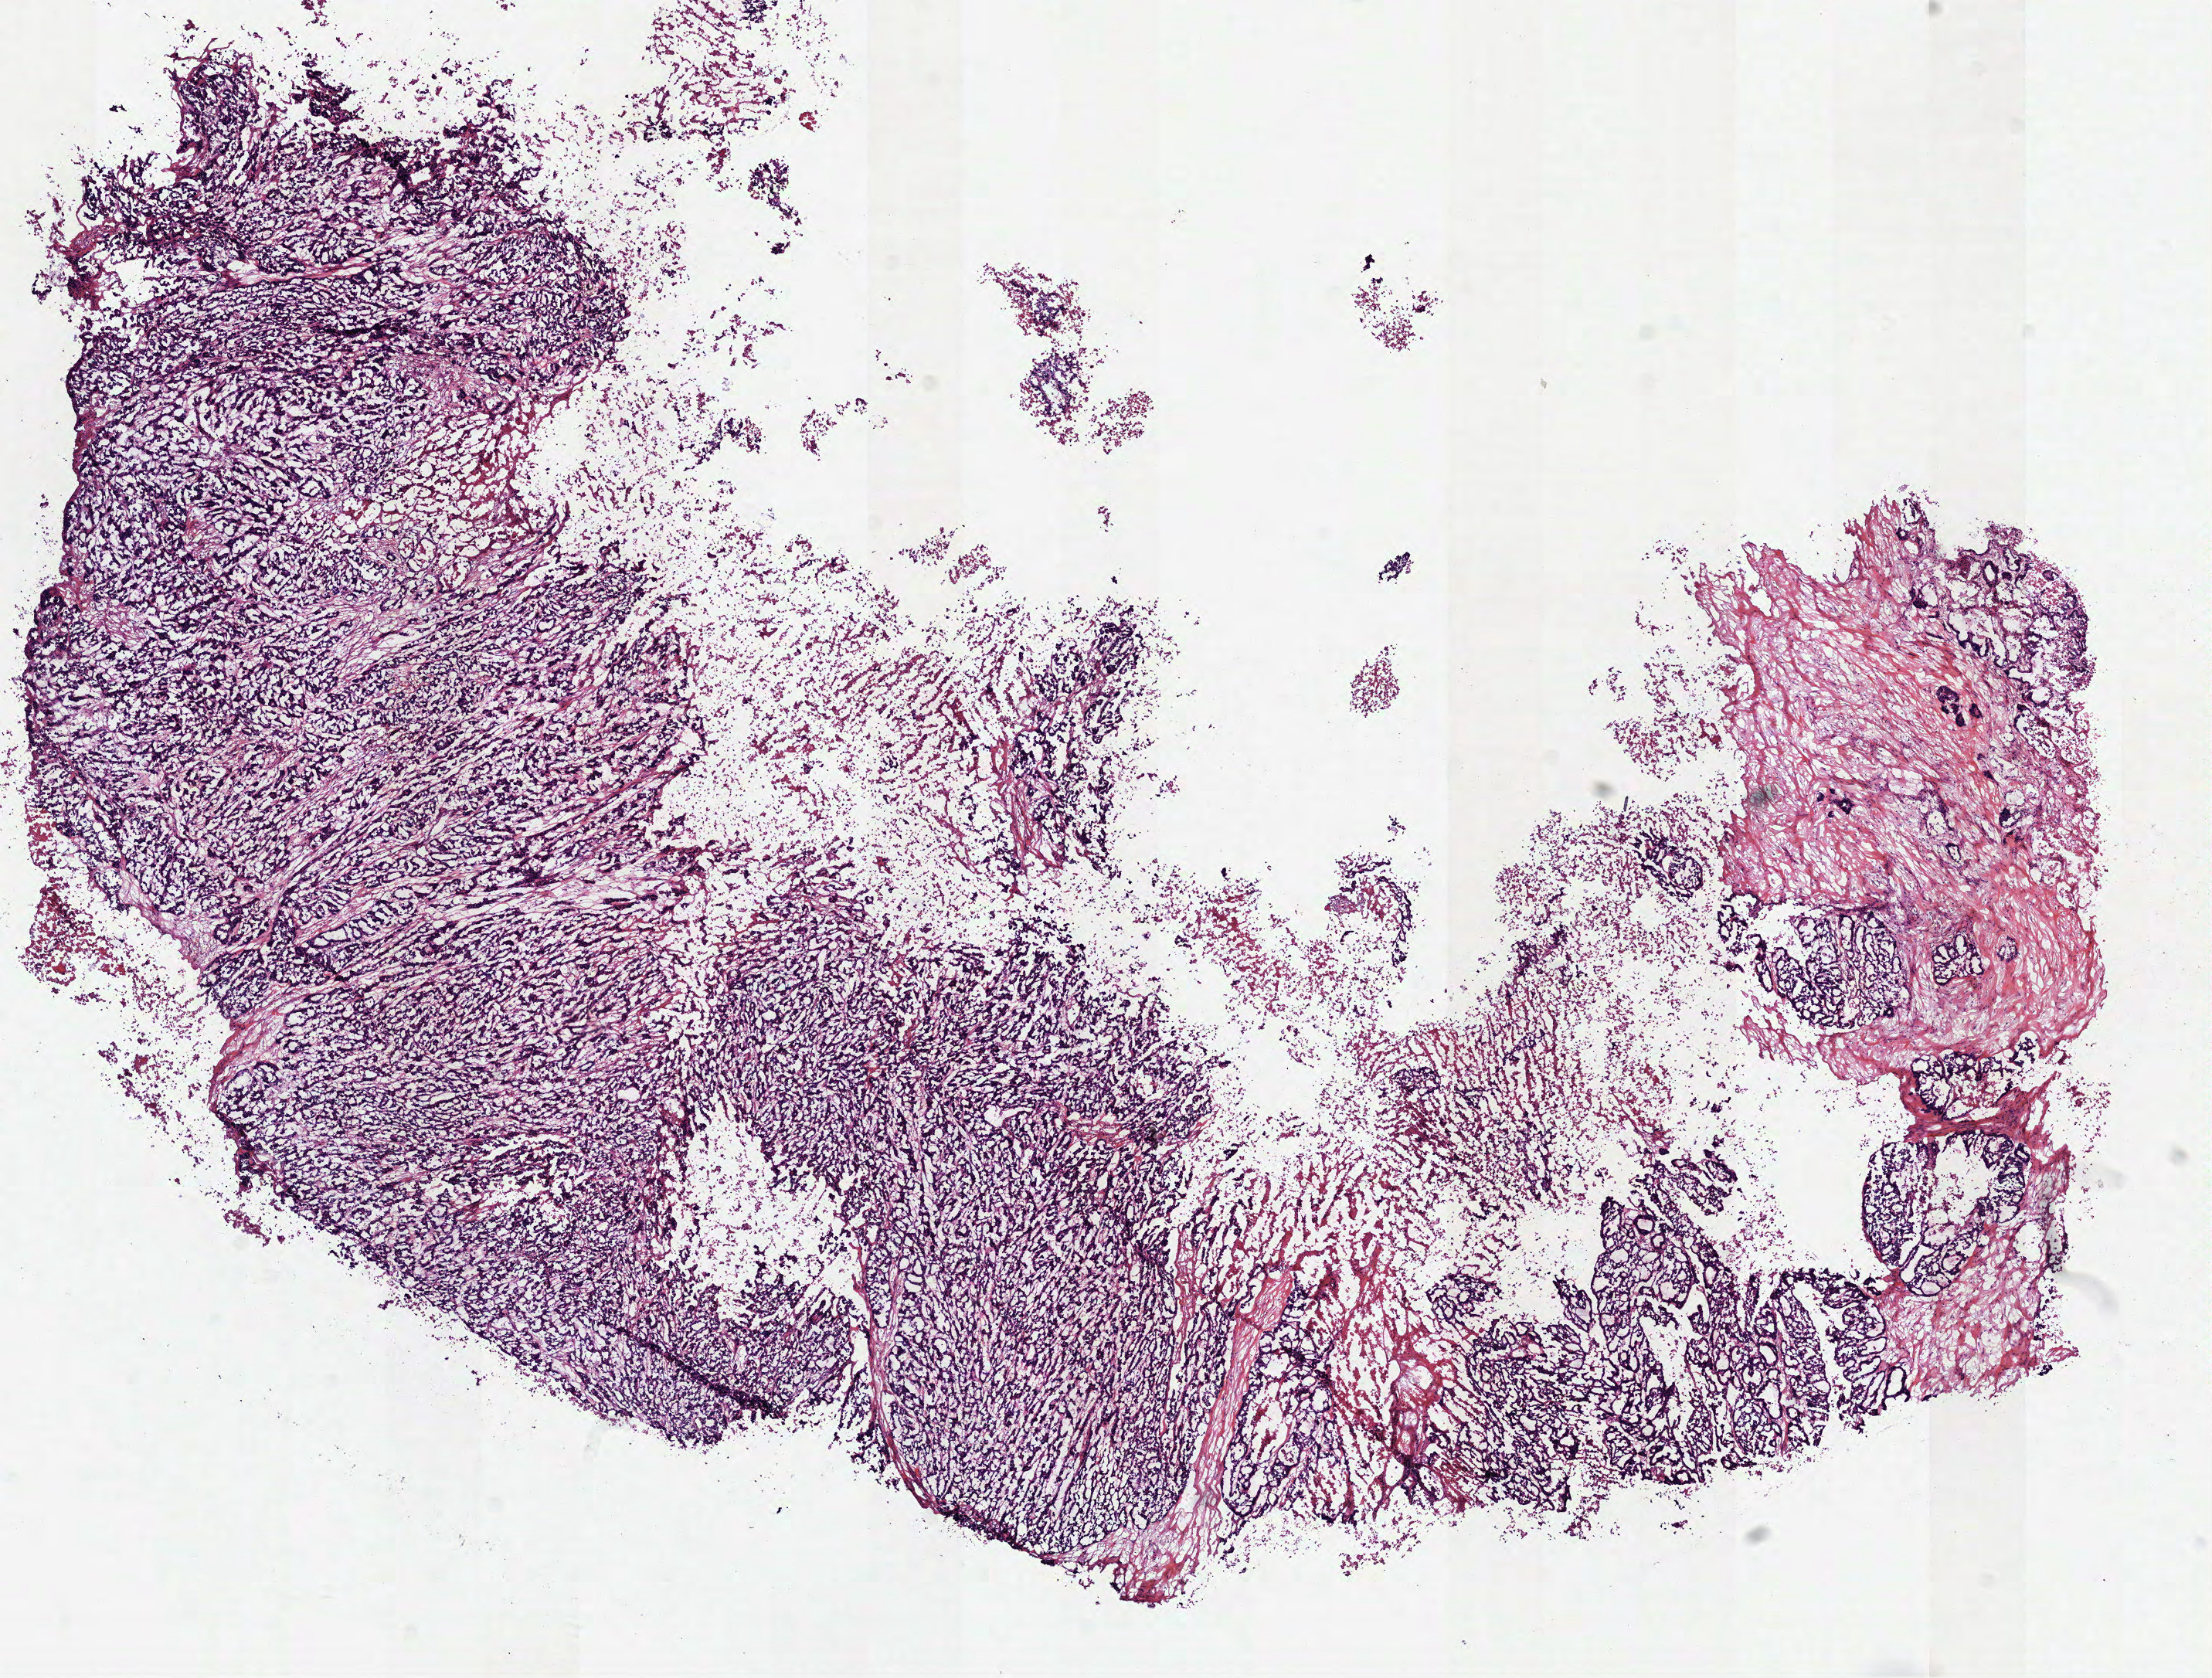
Digitized Hematoxylin and eosin (H&E) stained tissue section (whole slide), whole scanned area (about 11.5 x 8.8 mm) shown as a low-resolution overview; frozen section from the top of the tissue portion; primary tumour sample from the stomach. Patient: male, age at initial diagnosis 59 years. Histologic grade: G3 (poorly differentiated). Slide review estimates, as recorded: tumour cells 72%, tumour nuclei 85%, normal cells 0%, stromal cells 10%, necrosis 18%.
Lymph nodes positive (case pathology): 5 of 5 examined. AJCC pathologic stage: IIIA. Diagnosis: Adenocarcinoma, NOS (fundus of stomach).